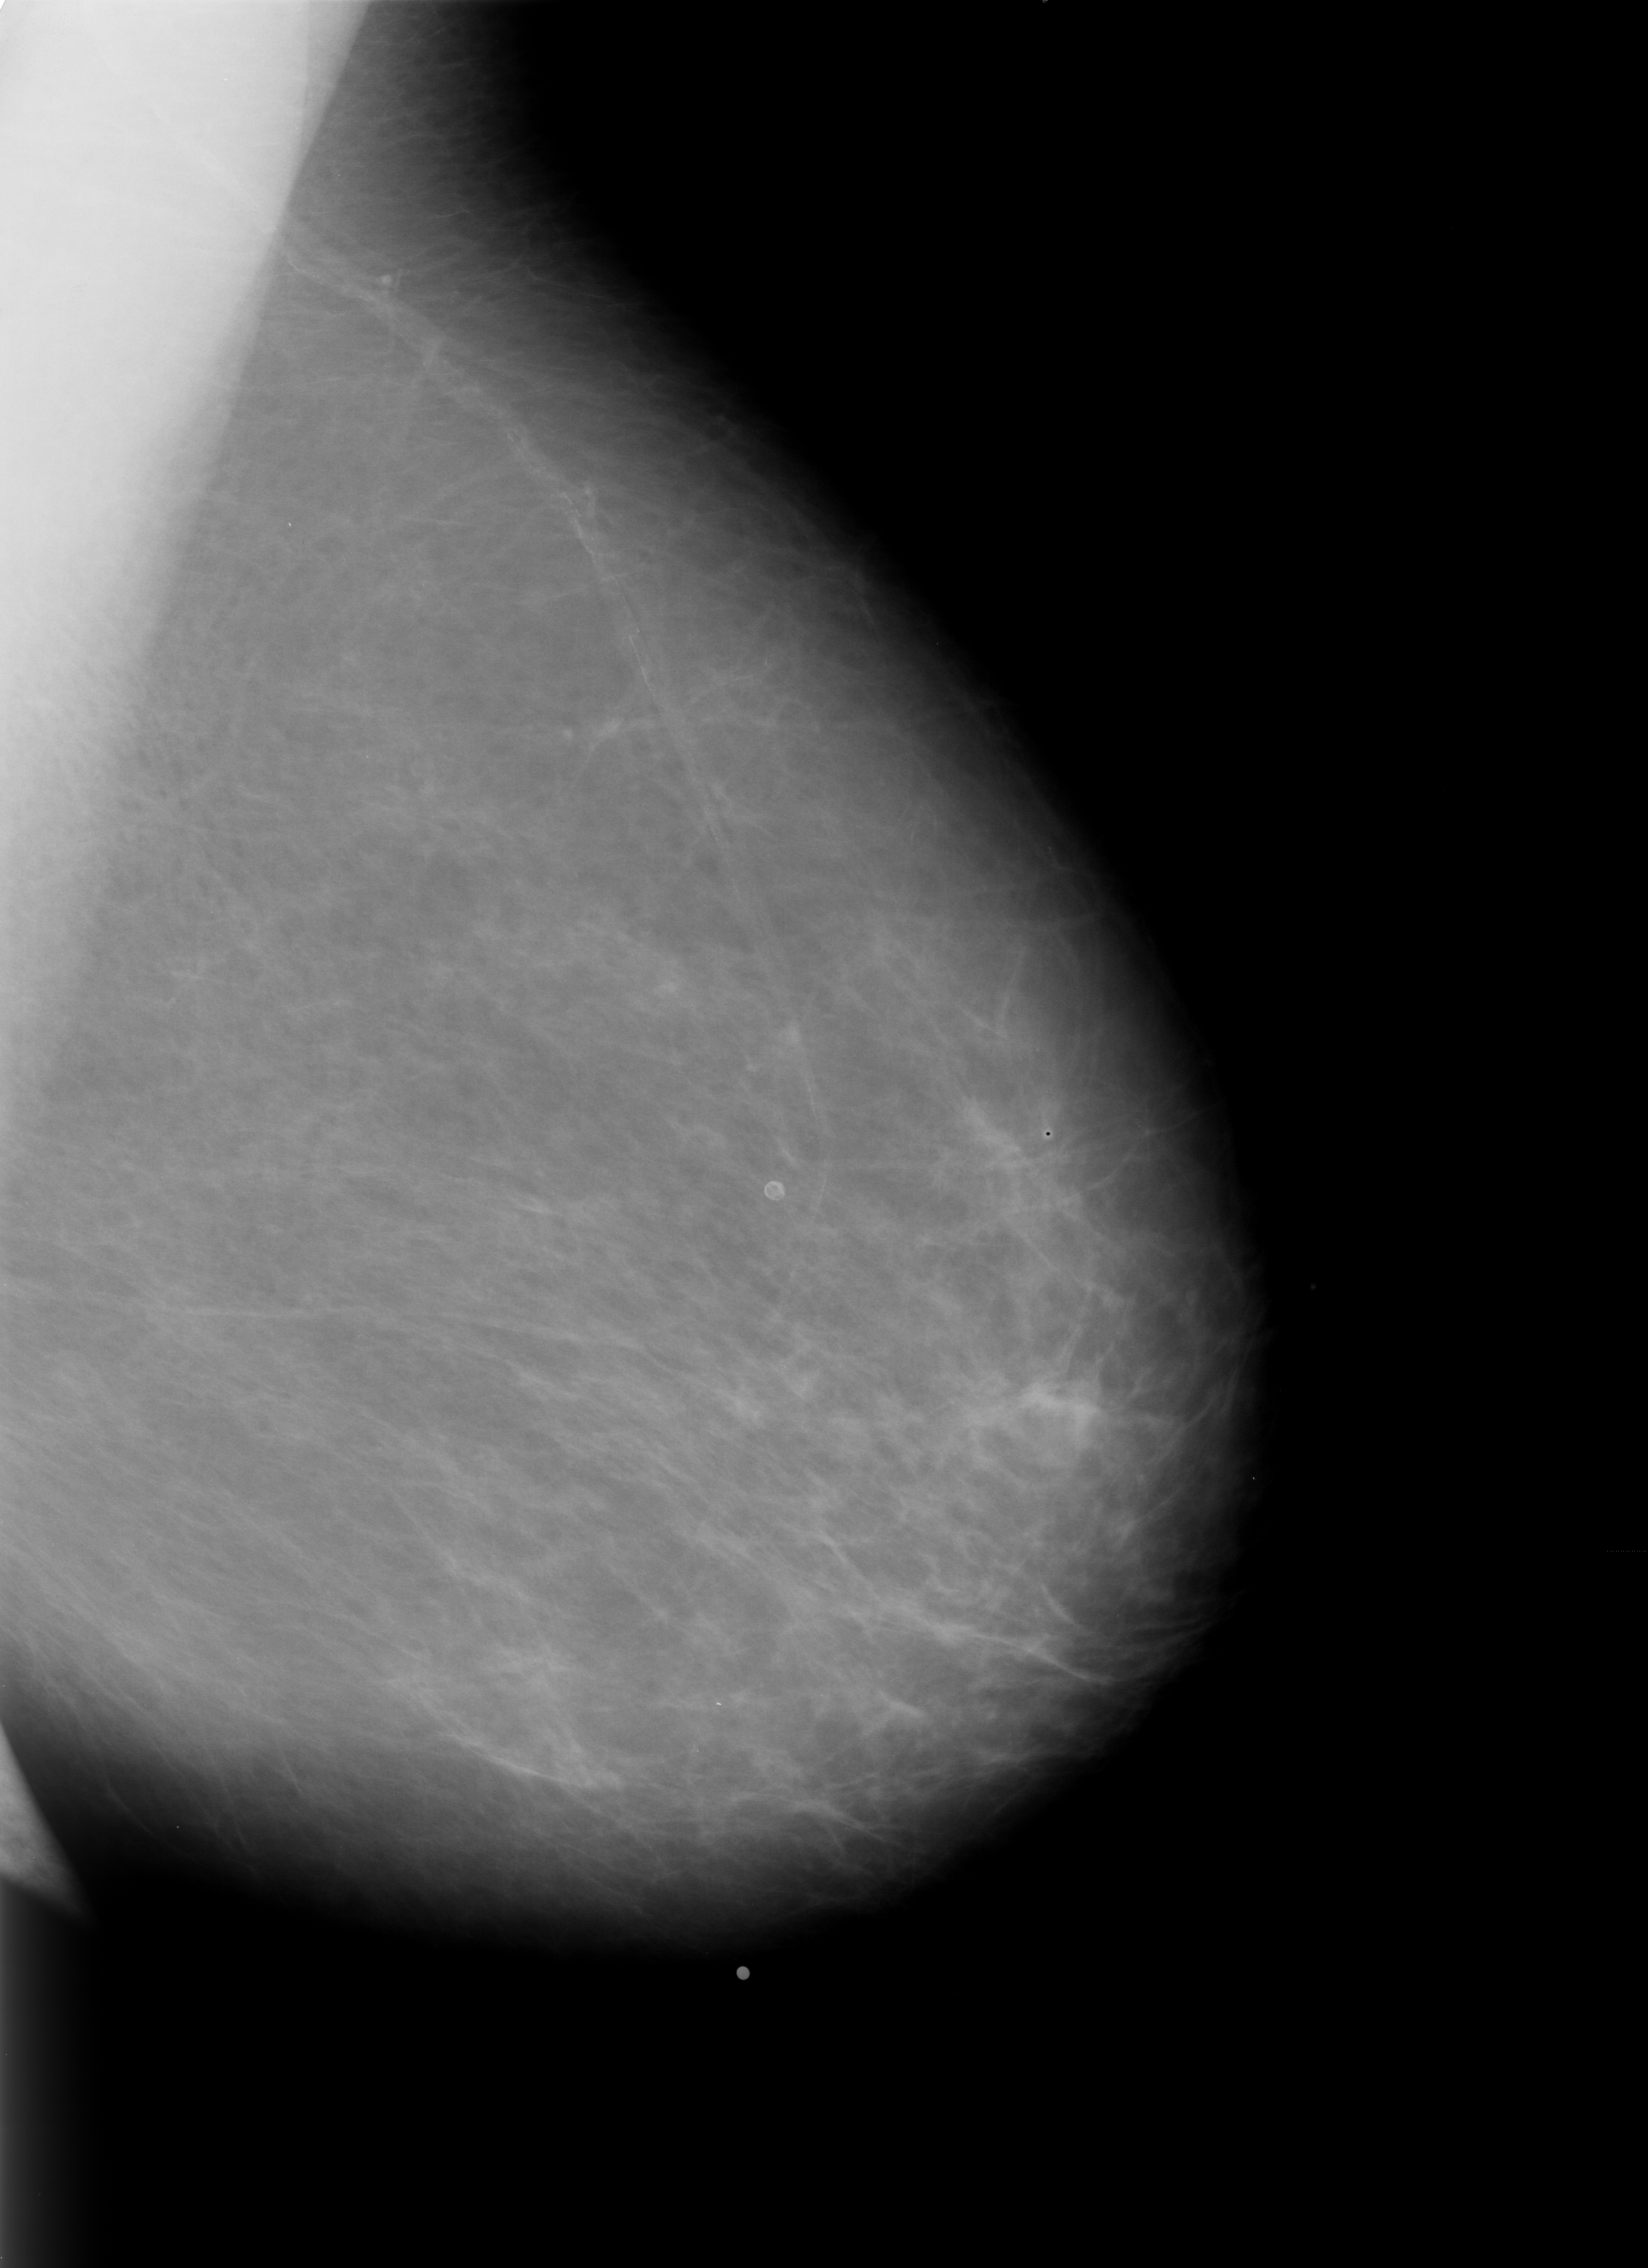
Digitized screen-film mammogram; left breast; MLO view; BI-RADS breast density category 1 (scale 1–4); 1648 × 2268 image matrix.
Marked abnormalities (boxes around the expert regions of interest):
- calcifications, morphology lucent centered; BI-RADS assessment category 2; benign; no additional work-up was recommended (outcome (as recorded, no biopsy): benign without callback): bounding box (x1, y1, x2, y2) in pixels: (756, 1170, 790, 1211)